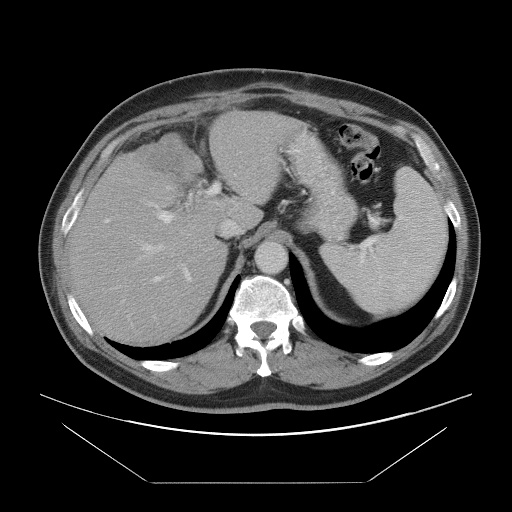
Contrast-enhanced abdominal CT, one axial slice. Soft-tissue window (W 400 / L 40 HU). 5 mm slice thickness. 512 × 512 image matrix. Male patient, age 62 years. From the clinical record (not read from this slice): diagnosis: colorectal cancer liver metastases, imaged before liver resection; multiple liver metastases: no.
Outlined on this slice (expert manual segmentation):
- hepatic veins: bounding box [x1, y1, x2, y2] px = [130, 185, 243, 264]
- liver: [71, 112, 292, 343]
- planned liver remnant (the part of the liver to remain after resection): [71, 172, 232, 342]
- portal vein (with intrahepatic branches): [105, 175, 236, 282]
- liver metastasis: [141, 141, 181, 177]